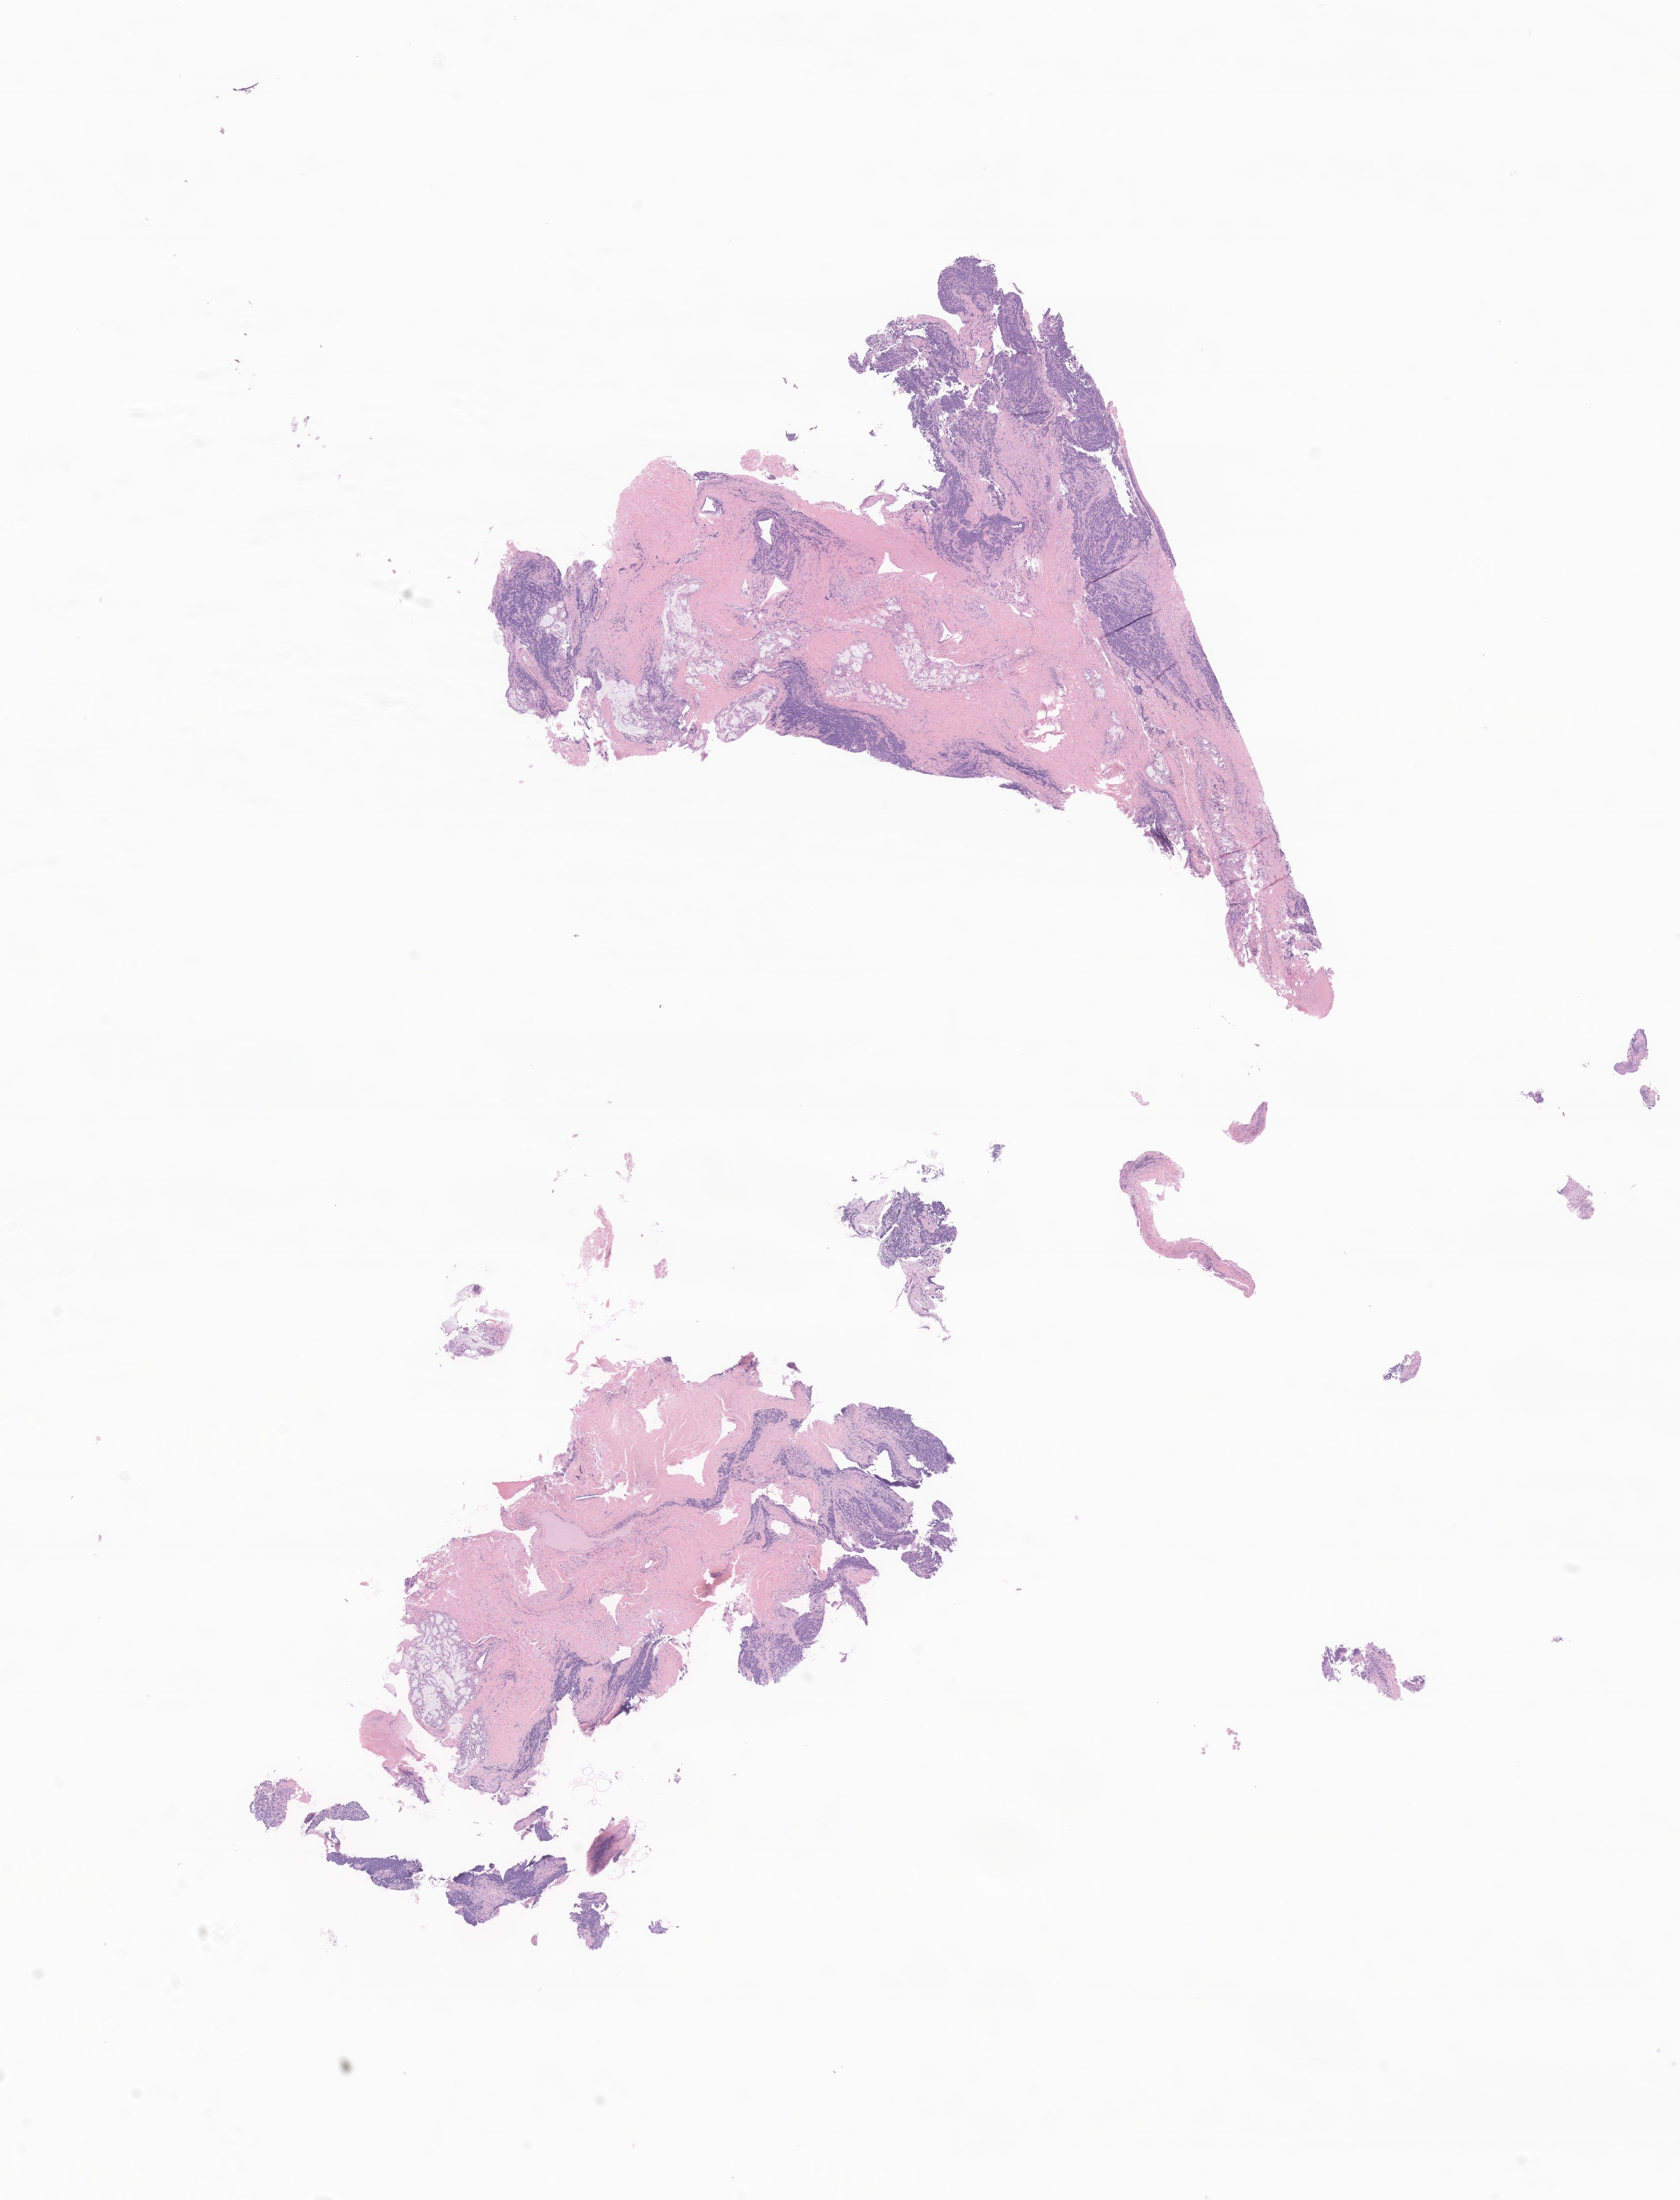
Whole-slide image, hematoxylin and eosin (H&E) stain of tumor tissue from the soft tissues of head and neck — whole scanned area (about 12.2 x 16.0 mm) shown as a low-resolution overview; FFPE section. Patient: male, age 73 months (6 years 1 month).
Recorded diagnosis: Embryonal rhabdomyosarcoma, NOS.